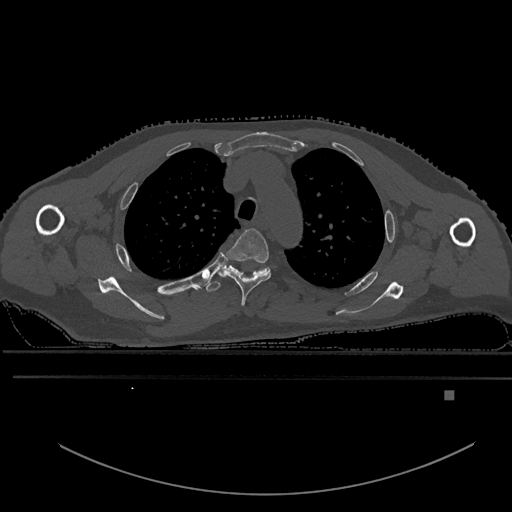
CT including the spine, one axial slice. Slice 439 of 969 in the series (ordered by position). Bone window (W 1800 / L 400 HU). 0.5 mm slice thickness. 512 × 512 image matrix, field of view 456 × 456 mm. Male patient, age 82 years. Case-level facts recorded for this patient, not image findings: primary cancer: prostate; vertebrae with lytic lesions (as recorded): T11, T9, T8, T2.
Annotated regions visible in this slice (semi-automatic segmentation, software-assisted and operator-edited):
- T3 vertebra: bounding box <218,228,271,306> (left, top, right, bottom; pixels)
- T4 vertebra: <206,261,270,292>